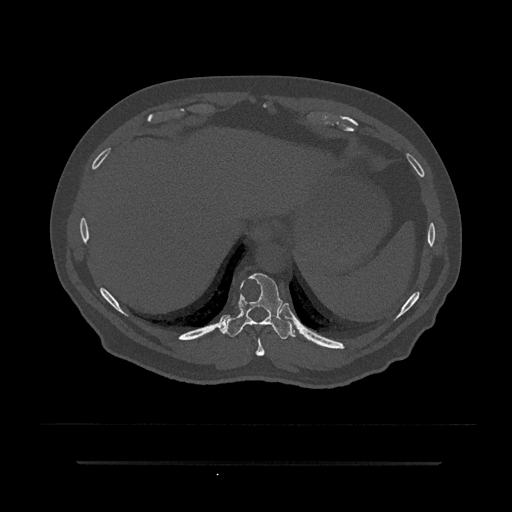
CT including the spine, one axial slice. Position 336 of 797 along the scan axis. 120 kVp. Bone window (W 1800 / L 400 HU). 0.5 mm slice thickness. 512 × 512 image matrix, field of view 464 × 464 mm. Male patient, age 59 years. From the clinical record (not read from this slice): primary cancer: bile ducts; vertebrae with lytic lesions (as recorded): T10.
Structures marked on this image (semi-automatic segmentation, software-assisted and operator-edited):
- T10 vertebra: box from (x=224, y=273) to (x=296, y=339) px
- T9 vertebra: (x=255, y=338)–(x=265, y=356)